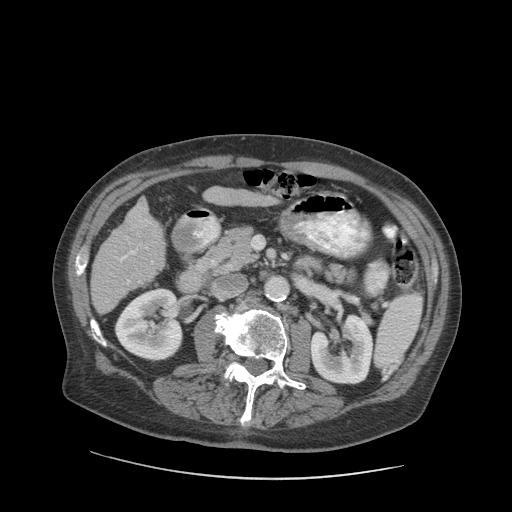
Contrast-enhanced abdominal CT (liver protocol), one axial slice; position 35 of 89 along the scan axis; reconstruction kernel STANDARD; 140 kVp; soft-tissue window (W 400 / L 40 HU); 2.5 mm slice thickness; 512 × 512 image matrix, field of view 420 × 420 mm. From the clinical record (not read from this slice): diagnosis: hepatocellular carcinoma (patient treated with transarterial chemoembolisation; whether this scan precedes or follows treatment is not stated here); TNM stage (as recorded): Stage-I; Child-Pugh class: A; tumour differentiation: moderately differentiated; tumour nodularity: uninodular.
Outlined on this slice (semi-automatically segmented with operator editing):
- liver parenchyma outside the tumour (the mass and vessels are separate outlines, so this box may not span the whole liver): bounding box [x1, y1, x2, y2] px = [90, 200, 164, 314]
- mass: [121, 211, 163, 248]
- liver vessels: [115, 247, 153, 284]